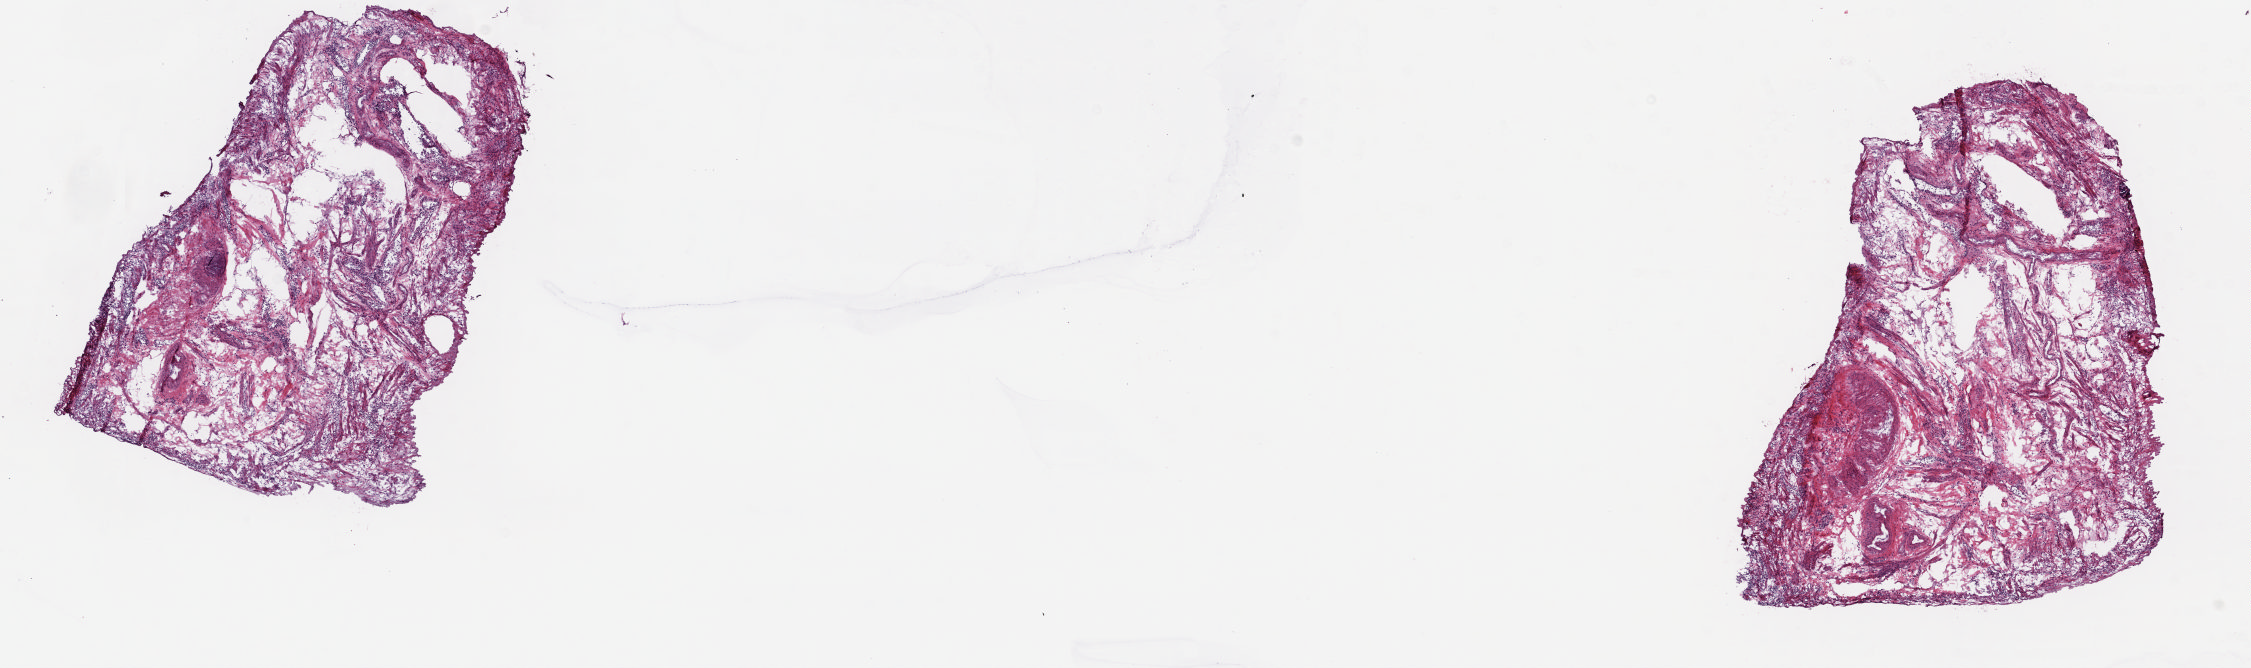
H&E whole-slide image — a low-resolution overview of the entire scanned area, about 17.9 x 5.3 mm (slide scanned at 20x); frozen section from the top of the tissue portion; sample: solid tissue normal (non-tumour tissue), uterus. Female, age 69 years at initial diagnosis. Composition of this section per pathologist review: tumour cells 0%, normal cells 100%.
* this section: solid tissue normal (non-tumour) sample from the same patient
* patient diagnosis: Endometrioid adenocarcinoma, NOS (endometrium)